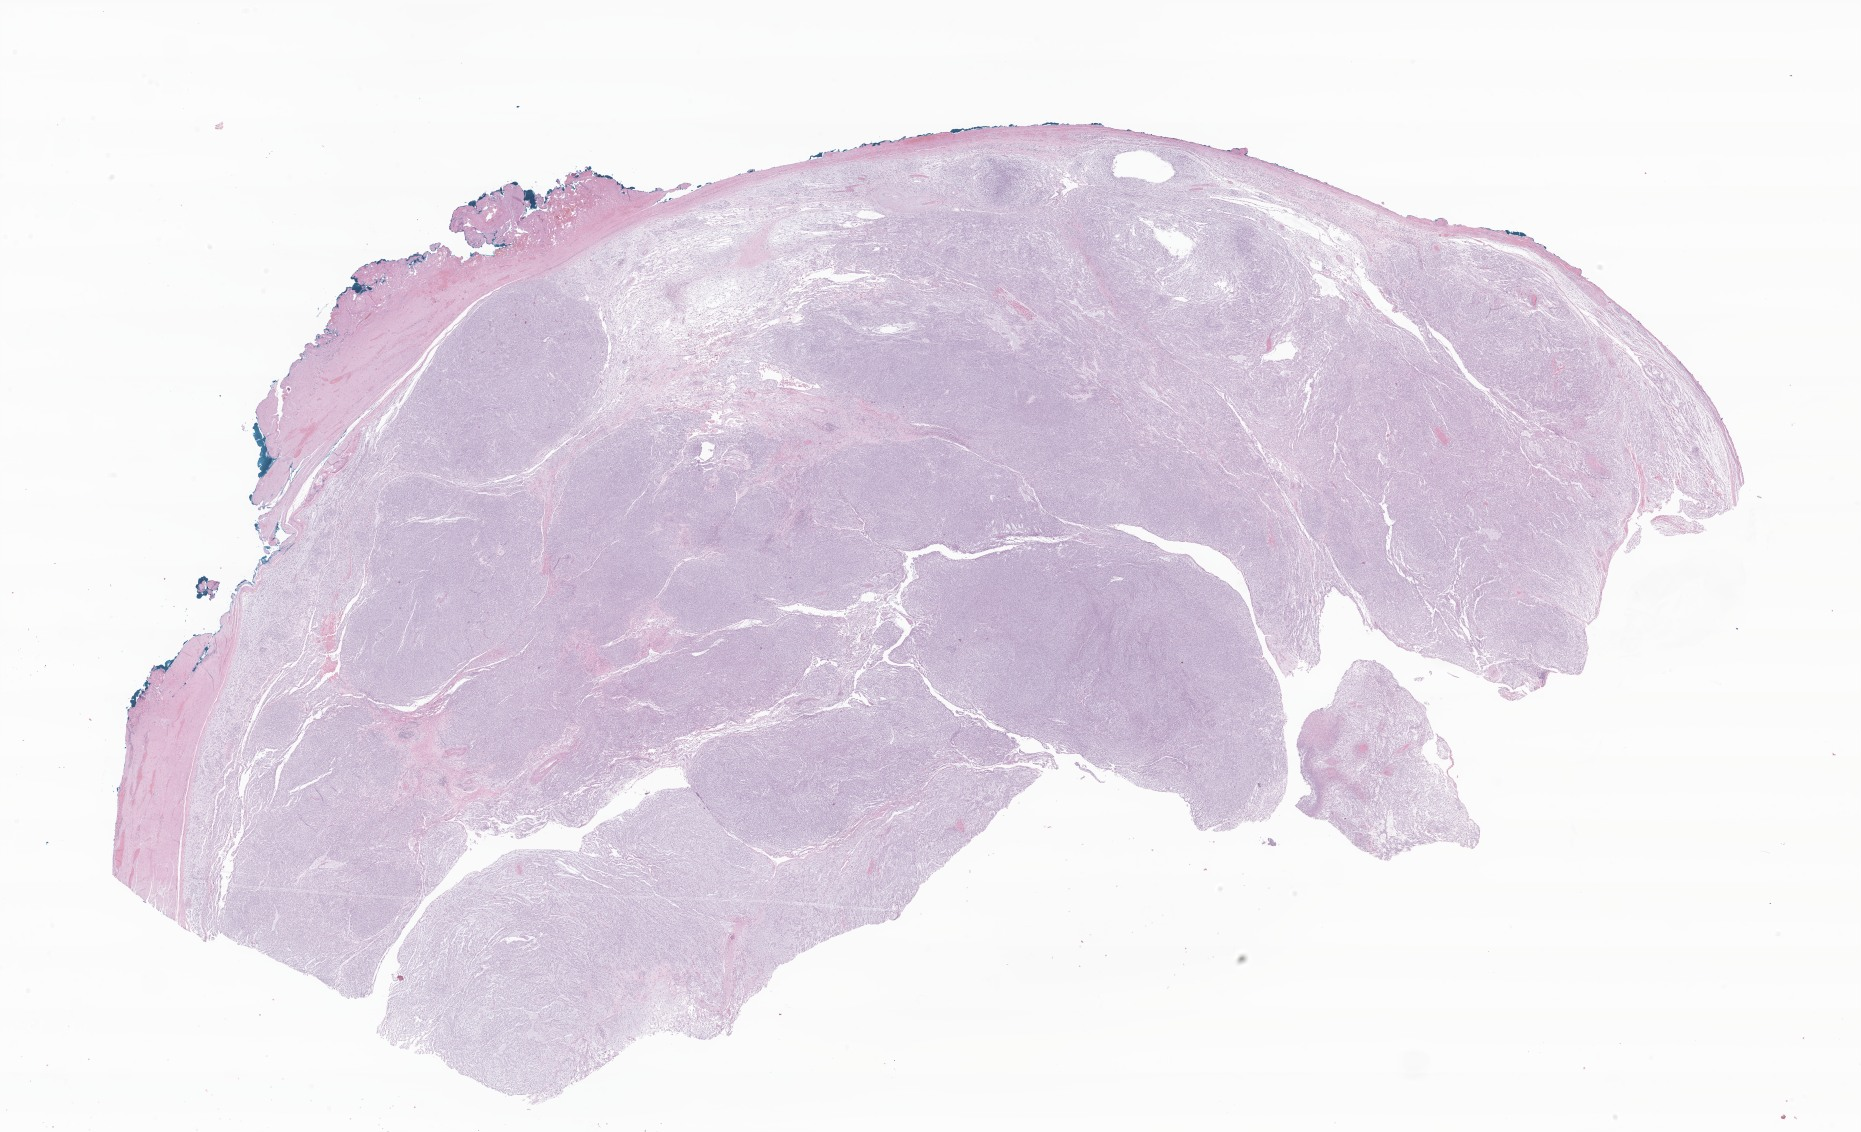
Haematoxylin and eosin whole-slide image of tumor tissue from the body of stomach, low-resolution overview of the scanned area, about 31.4 x 19.1 mm; formalin-fixed, paraffin-embedded (FFPE) tissue. Patient male; age 225 months (18 years 9 months).
Diagnosis: Gastrointestinal stromal tumor.